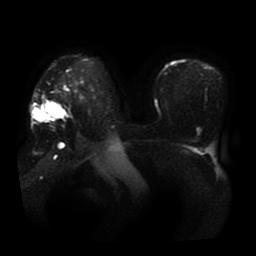
Breast MRI, one axial slice; slice 29 of 41 in the series (ordered by position); diffusion-weighted series; image 2 of 4 stored at this slice position (different b-values; order by instance number); 1.5 T; 5 mm slice thickness; 256 × 256 image matrix, field of view 360 × 360 mm. Female patient.
Outlined on this slice (outlined manually by an expert reader):
- tumour on diffusion-weighted imaging: bounding box (x1, y1, x2, y2) in pixels: (30, 107, 60, 124)